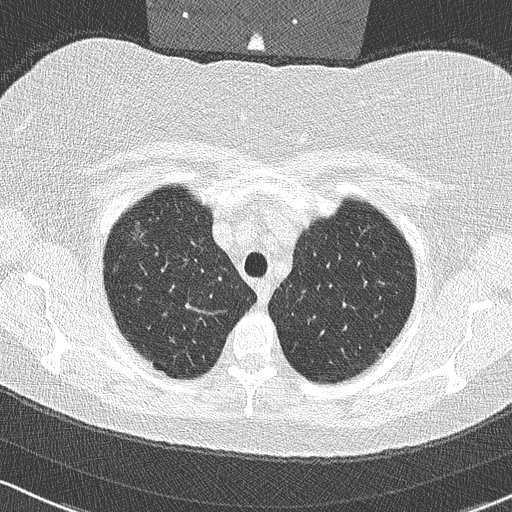
Axial slice from a low-dose chest CT screening exam. Third screening round (two years after baseline). Lung window (W 1500 / L -600 HU). Lung (sharp) reconstruction kernel (B50f). 512 × 512 image matrix, field of view 320 × 320 mm. Female, age 58 years at enrolment. Former smoker at enrolment.
- Lesion marked by an expert reader, bounding box (x1, y1, x2, y2) in pixels: (121, 216, 162, 252).
- The screening reader recorded 2 non-calcified nodules or masses ≥4 mm on this exam (right upper lobe, right lower lobe); which of them this box marks is not recorded.
- Lung cancer was diagnosed 48 days after this screen: bronchiolo-alveolar adenocarcinoma, NOS, right upper lobe, well differentiated (G1), stage IA (AJCC 6th edition), 9 mm at pathology.